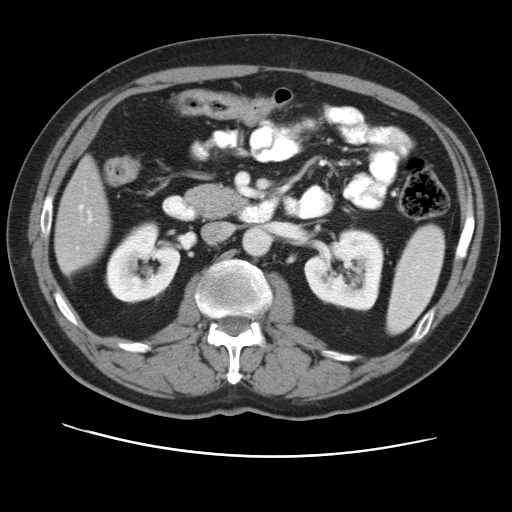
Contrast-enhanced abdominal CT, one axial slice. Slice 18 of 49 in the series (ordered by position). Reconstruction kernel STANDARD. 120 kVp. Intravenous contrast given. Soft-tissue window (W 400 / L 40 HU). 5 mm slice thickness. 512 × 512 image matrix, field of view 374 × 374 mm. Male patient, age 59 years. From the clinical record (not read from this slice): diagnosis: colorectal cancer liver metastases, imaged before liver resection; multiple liver metastases: yes; largest metastasis: 6.3 cm.
Annotated regions visible in this slice (outlined manually by an expert reader):
- hepatic veins: bounding box (x1, y1, x2, y2) in pixels: (80, 205, 83, 208)
- liver: (56, 160, 110, 270)
- planned liver remnant (the part of the liver to remain after resection): (63, 160, 110, 233)
- portal vein (with intrahepatic branches): (88, 213, 92, 221)